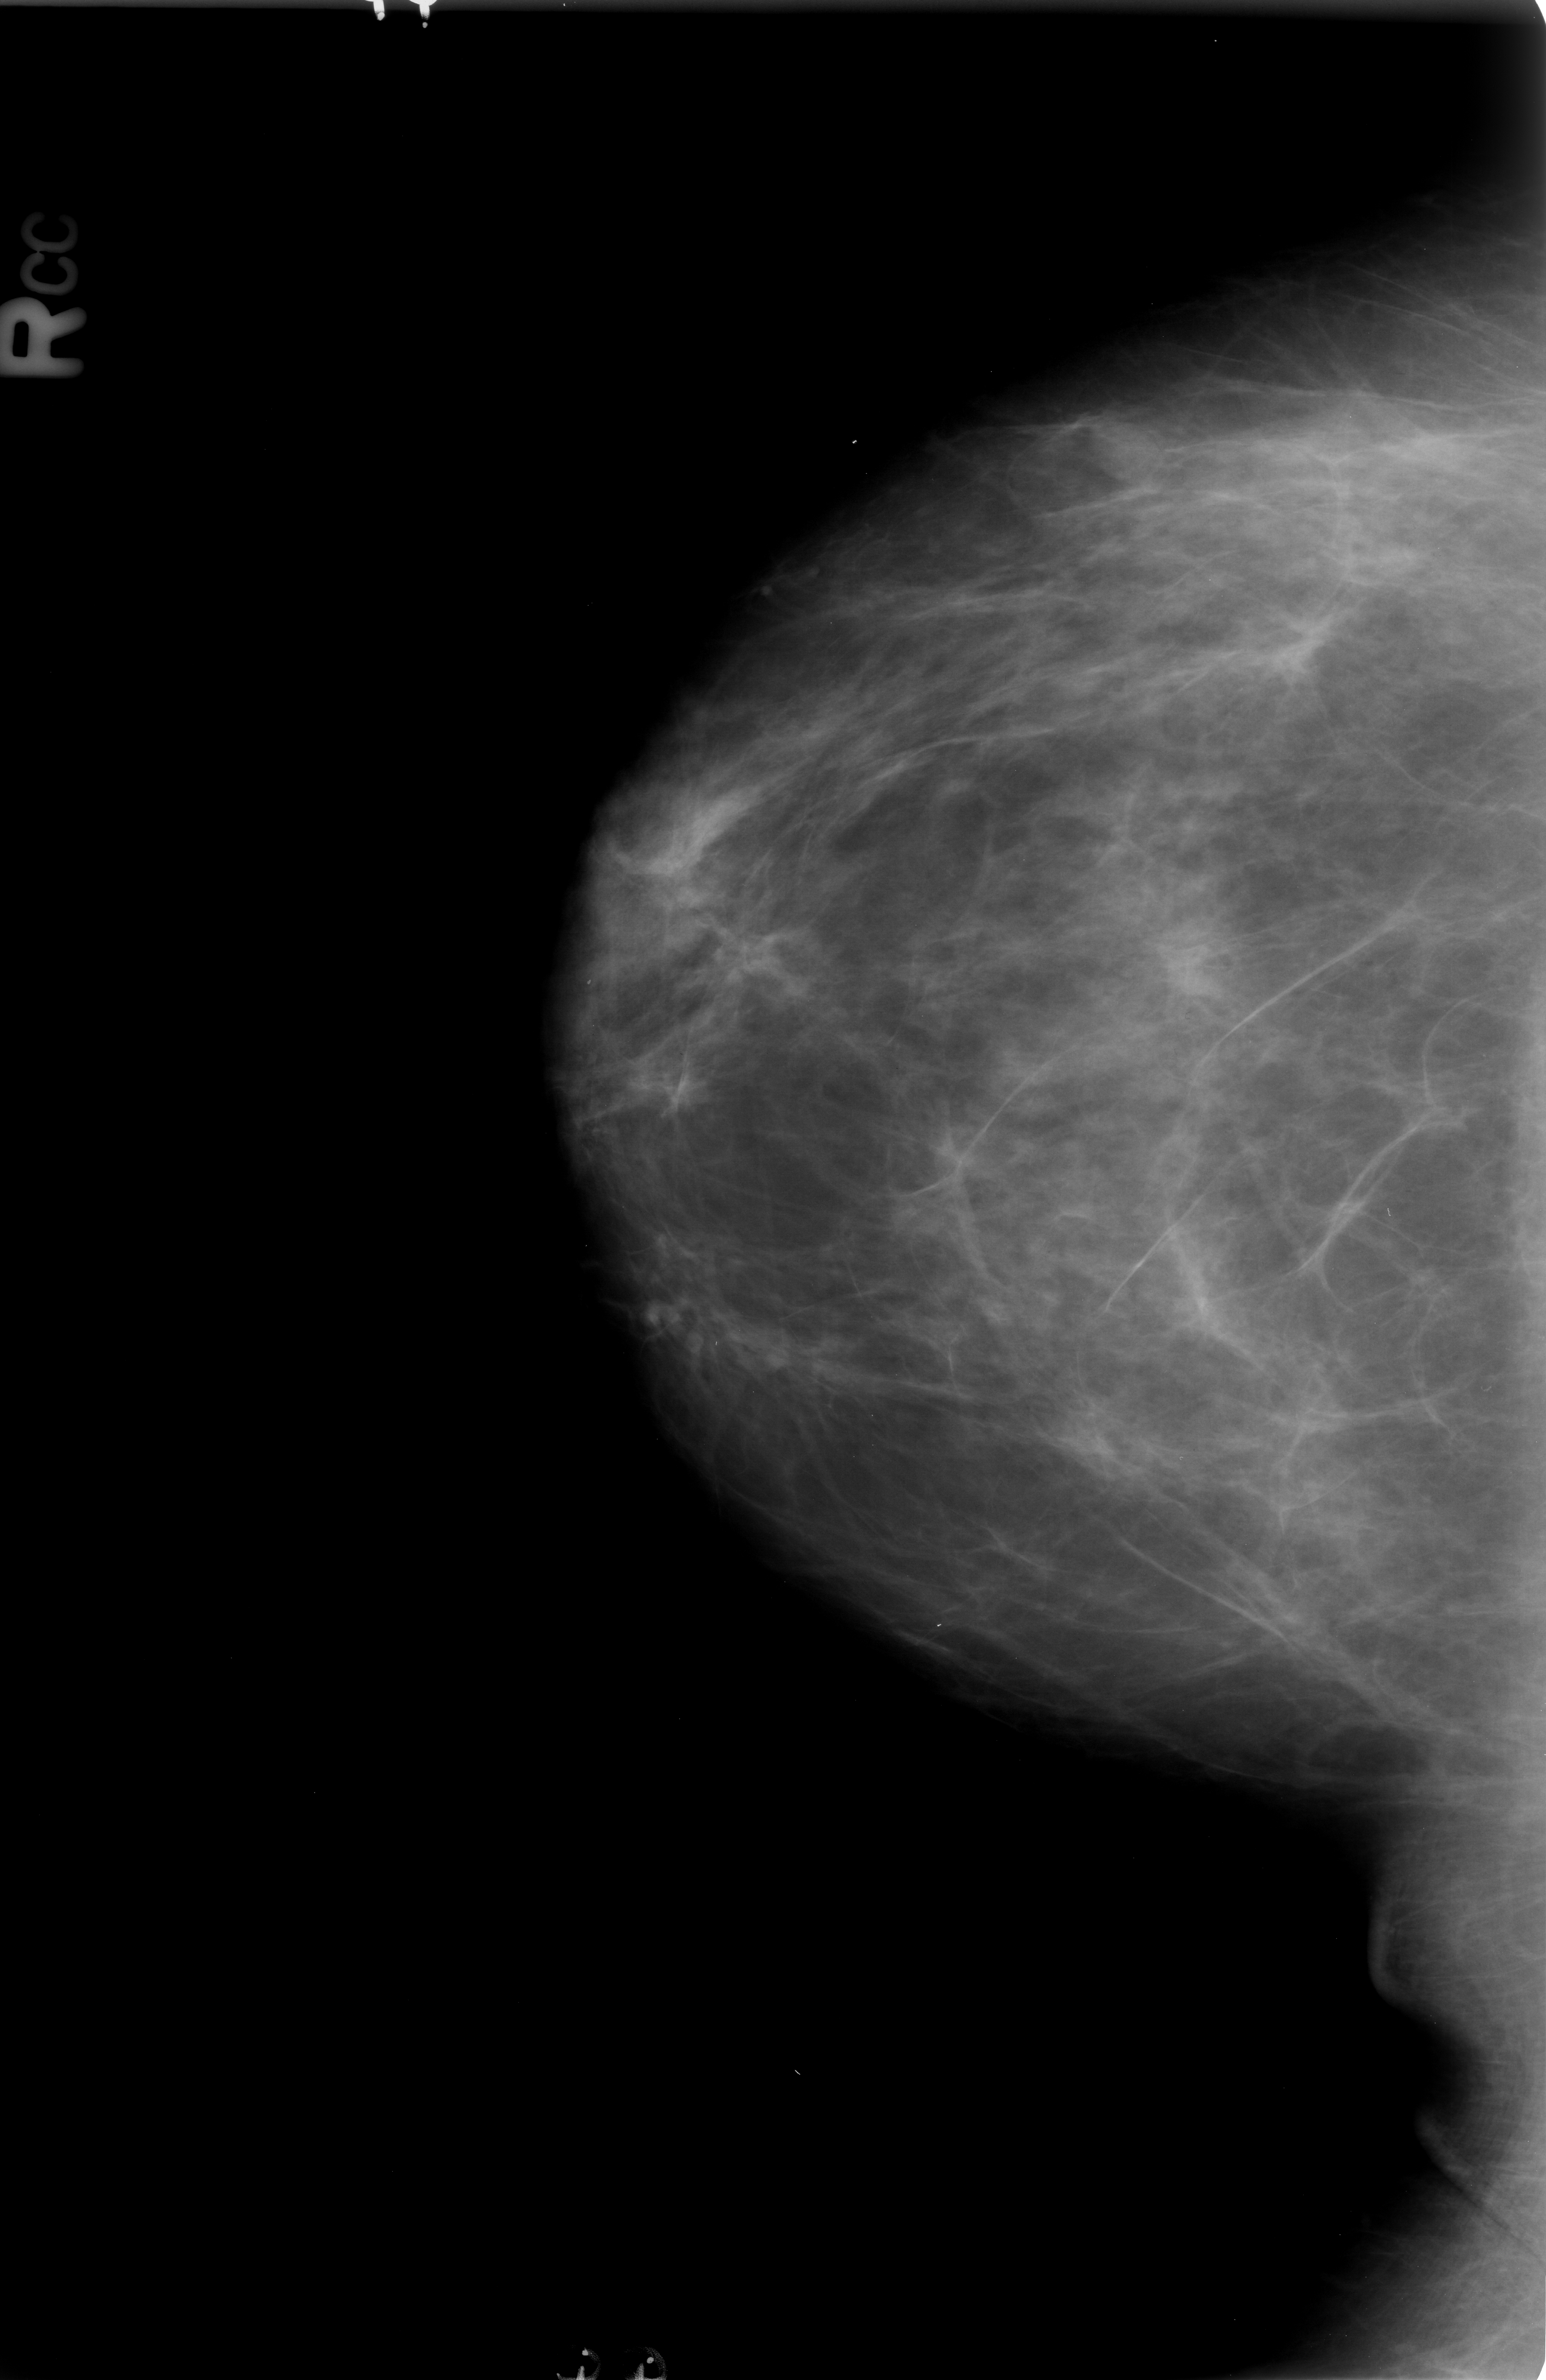
Digitized screen-film mammogram; right breast; CC view; BI-RADS breast density category 2 (scale 1–4); 1546 × 2380 image matrix.
Expert-marked regions of interest on this image (one box per marked abnormality):
- mass, shape oval, margins circumscribed / obscured; BI-RADS assessment category 4; subtlety rating 3 on a 1 (subtle) to 5 (obvious) scale; pathology result (as recorded, not read from the image): benign: bounding box (x1, y1, x2, y2) in pixels: (1103, 420, 1194, 484)